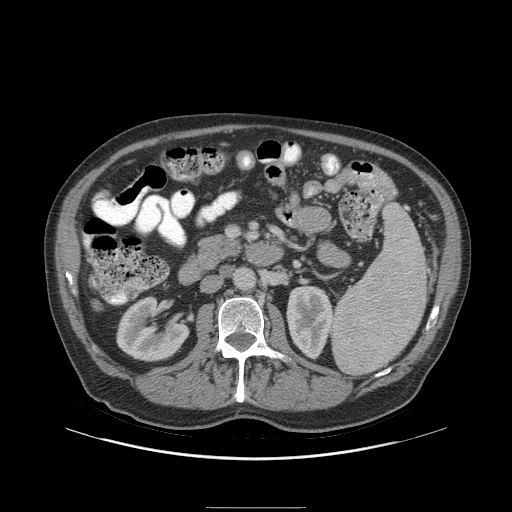
Contrast-enhanced abdominal CT (liver protocol), one axial slice. Position 24 of 105 along the scan axis. 140 kVp. Soft-tissue window (W 400 / L 40 HU). 512 × 512 image matrix. From the clinical record (not read from this slice): diagnosis: hepatocellular carcinoma (patient treated with transarterial chemoembolisation; whether this scan precedes or follows treatment is not stated here); TNM stage (as recorded): Stage-I; Child-Pugh class: A; tumour nodularity: uninodular.
Annotated regions visible in this slice (semi-automatically segmented with operator editing):
- liver parenchyma outside the tumour (the mass and vessels are separate outlines, so this box may not span the whole liver): bounding box <94,302,98,307> (left, top, right, bottom; pixels)